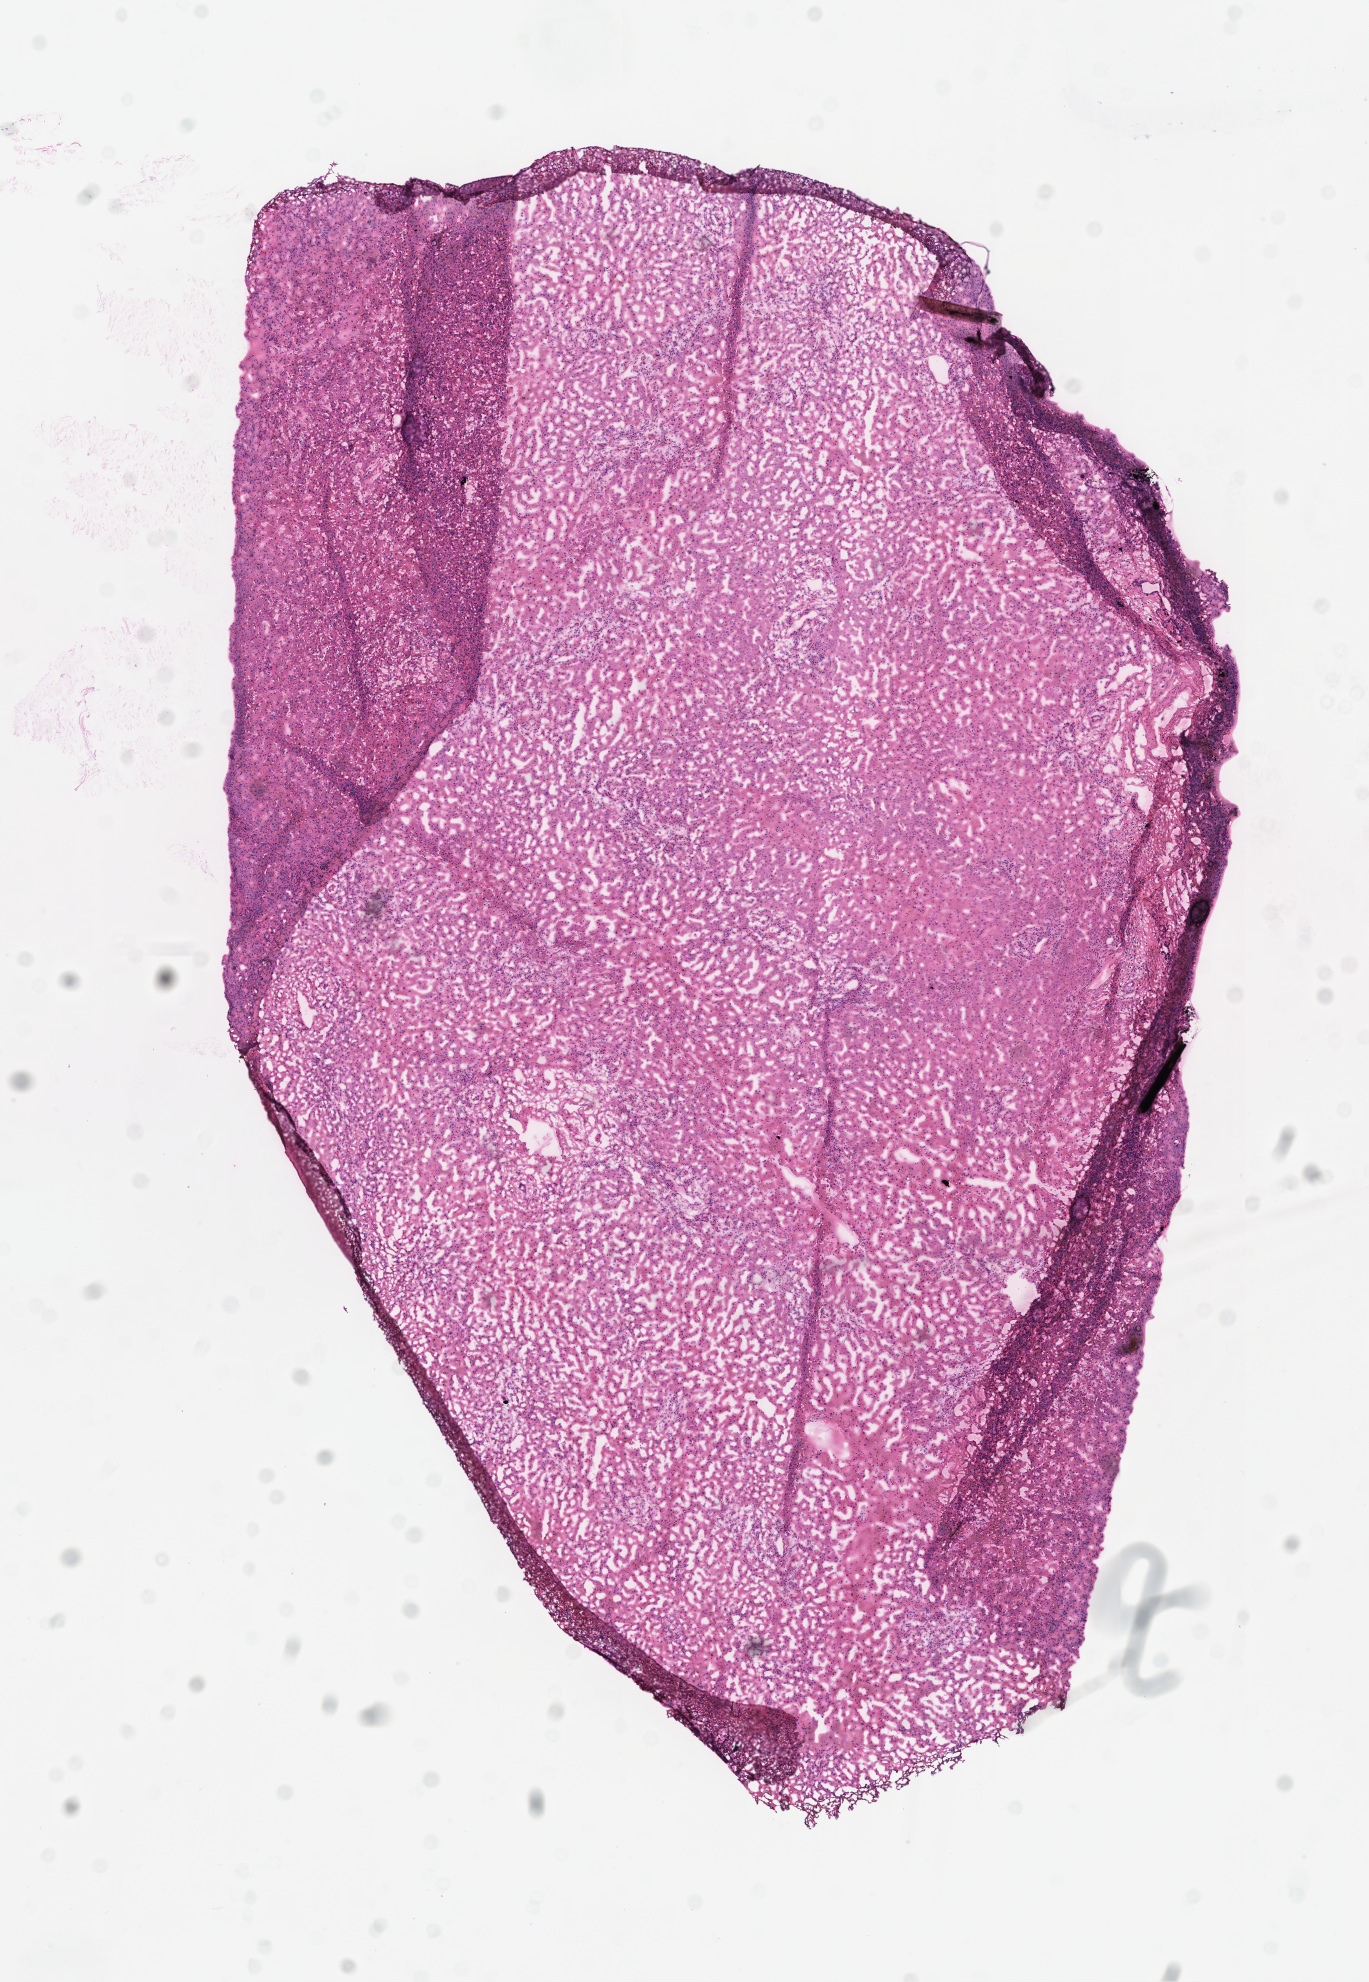
Digitized hematoxylin and eosin (H&E)-stained section, a low-resolution overview of the entire scanned area, about 5.5 x 8.0 mm, frozen section, normal-tissue sample (non-tumor) from a patient with adenocarcinoma, NOS, site: colon. Female patient; age at initial diagnosis 49 years.
This section: non-tumor tissue sample; the patient's diagnosis is given above.